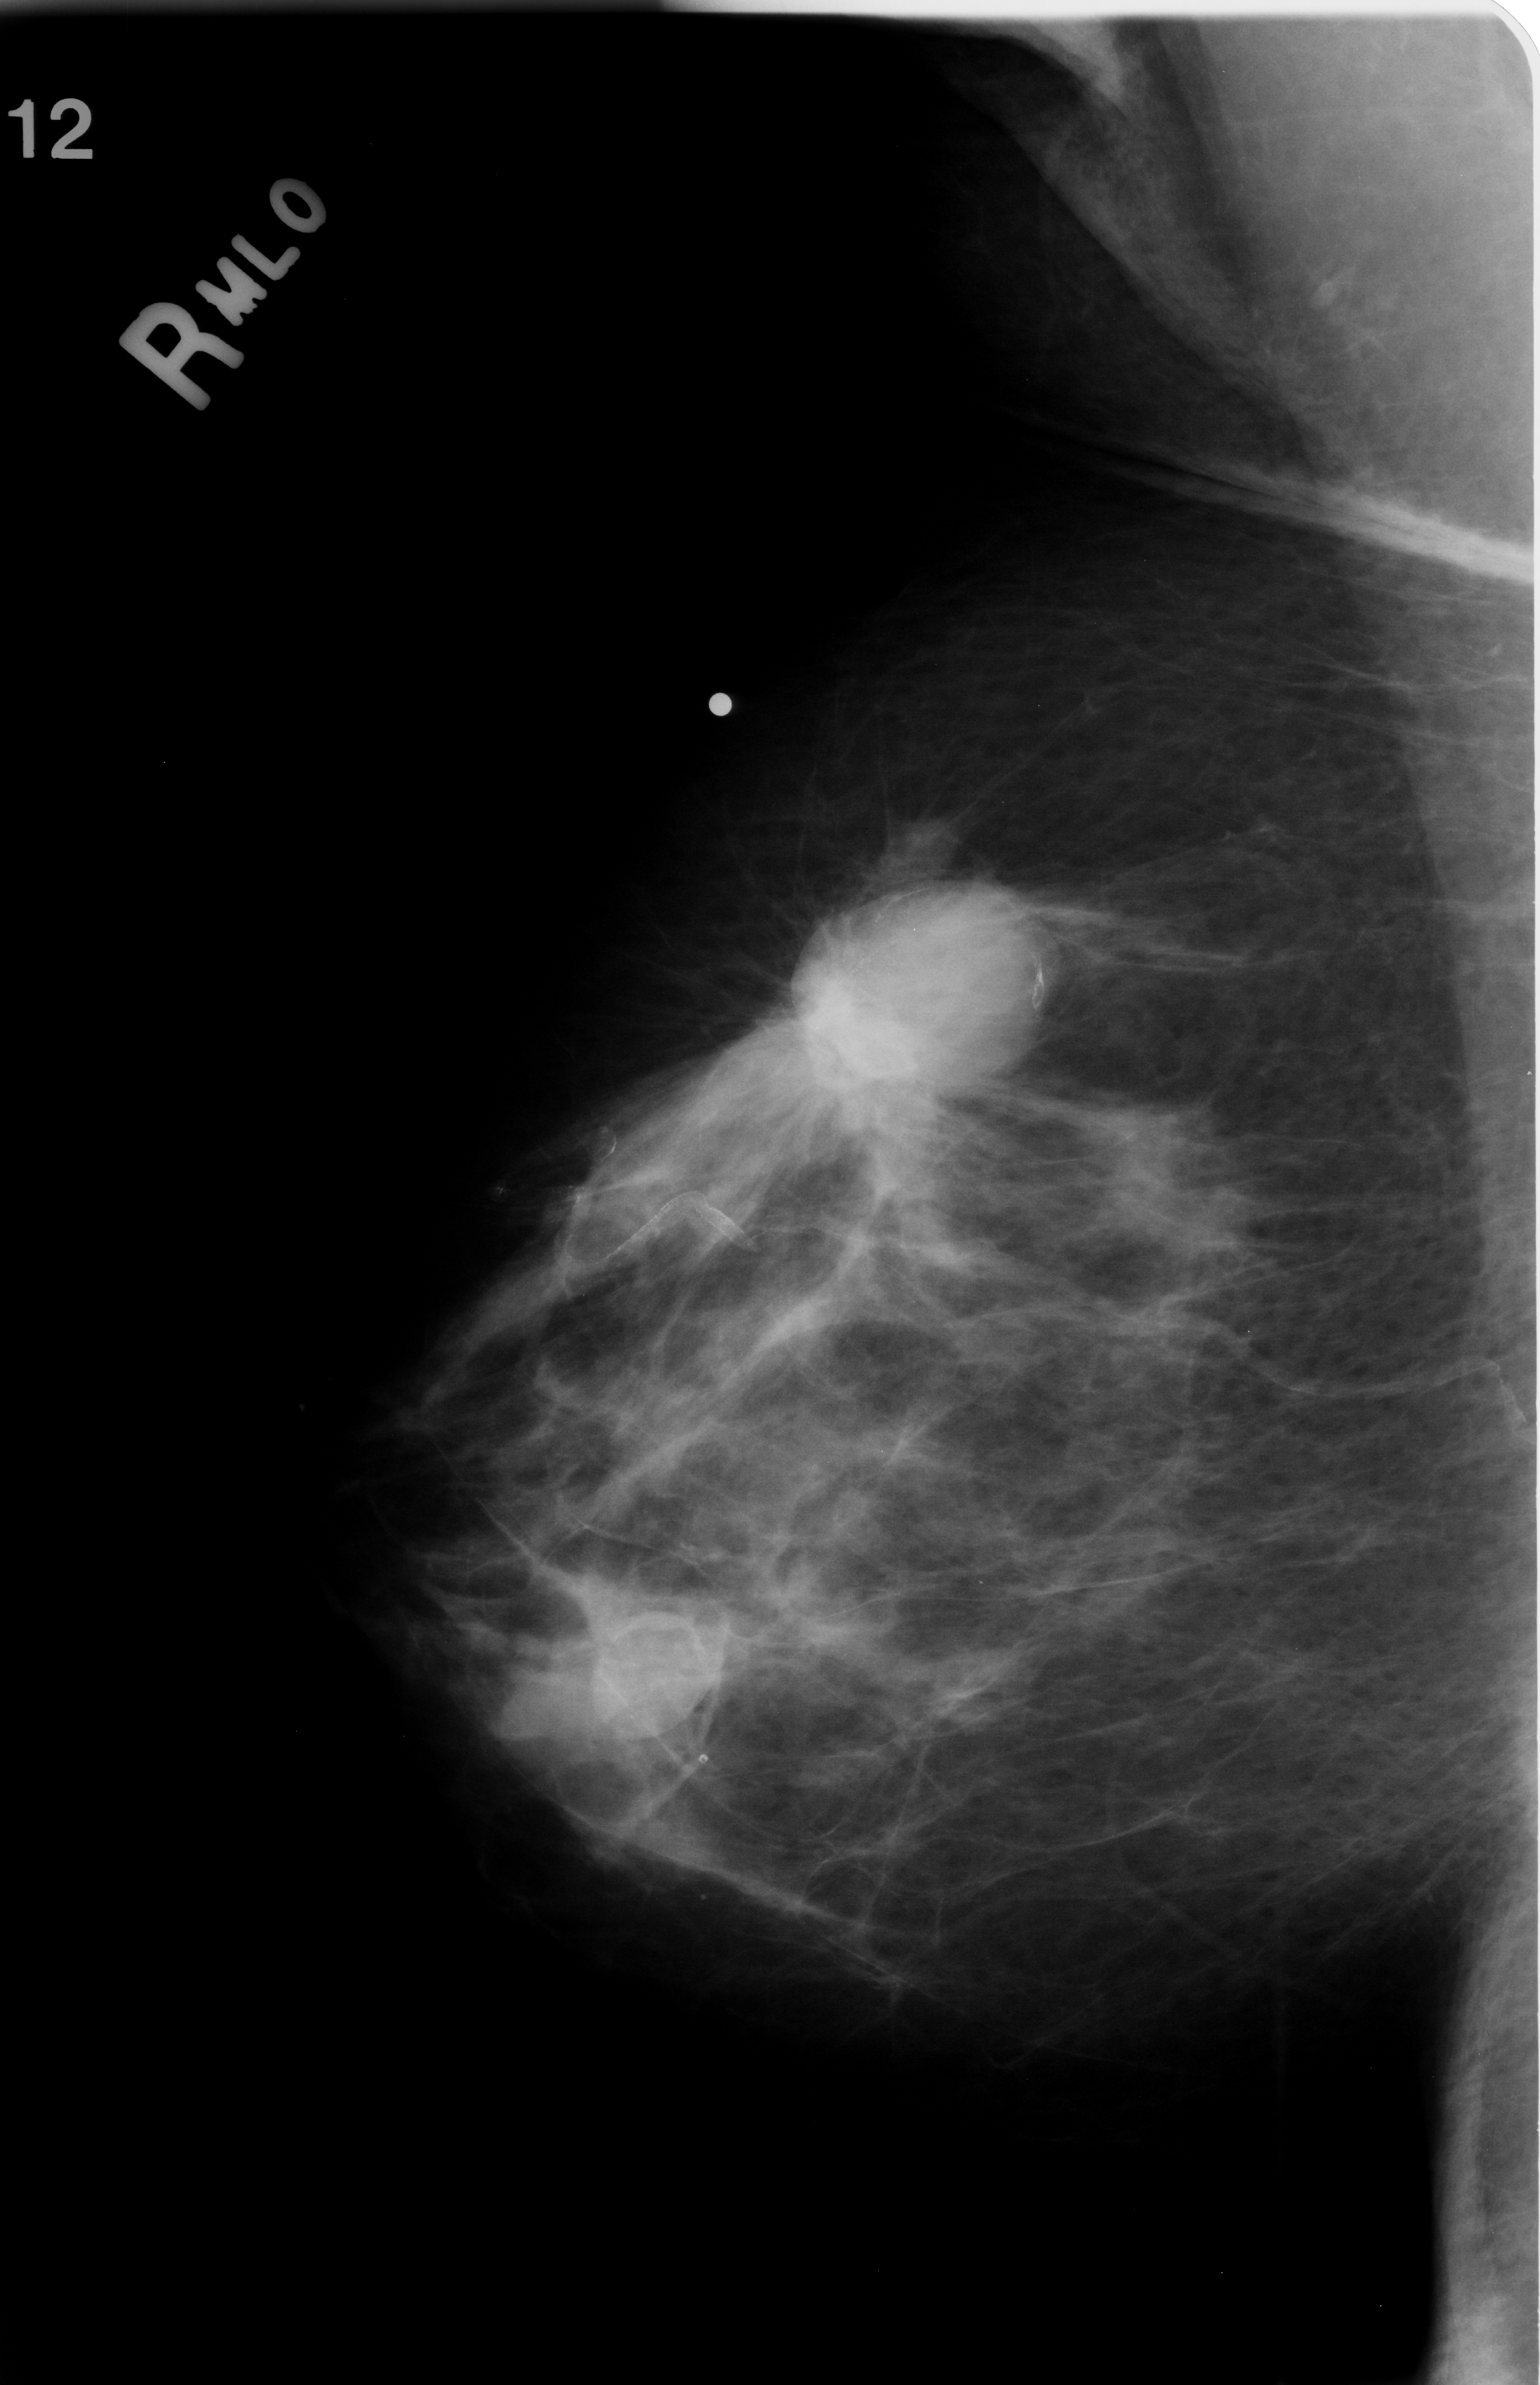
Scanned film-screen mammogram; right breast; mediolateral oblique (MLO) view; BI-RADS breast density category 2 (scale 1–4).
Abnormality record for this image: mass, shape lobulated, margins spiculated; BI-RADS assessment category 5; subtlety rating 5 on a 1 (subtle) to 5 (obvious) scale; pathology result (as recorded, not read from the image): malignant.